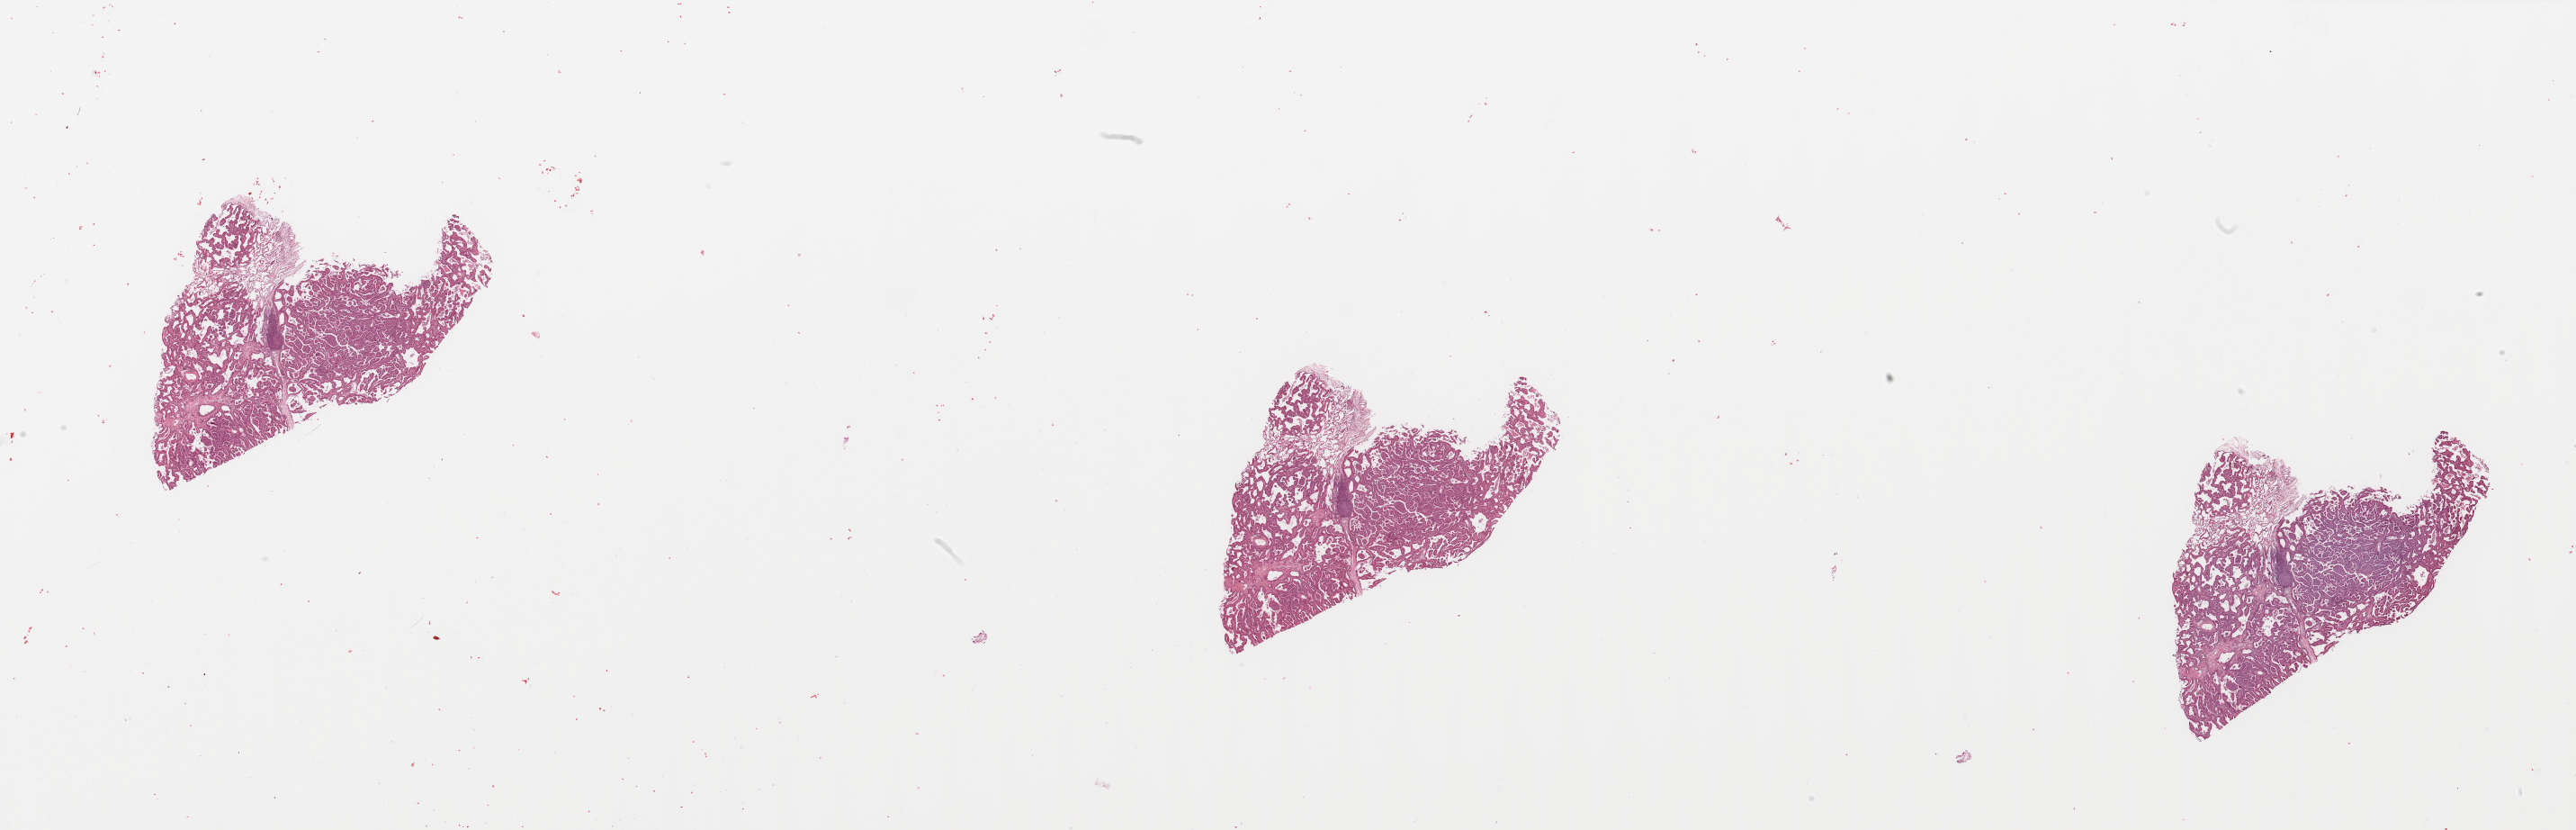
H&E-stained whole-slide image, shown as a low-resolution overview of the whole scanned area (about 45.3 x 14.6 mm, slide scanned at 20x), tumour tissue sample, sampled site: lung. Female, 66 y/o. Histologic grade: G1 (well differentiated). Pathologist review of this section (percent, as recorded): tumour nuclei 70%, necrosis 0%.
Diagnosis: Adenocarcinoma, NOS. Primary tumour site (as recorded): right lower lobe. AJCC pathologic stage: IIB.